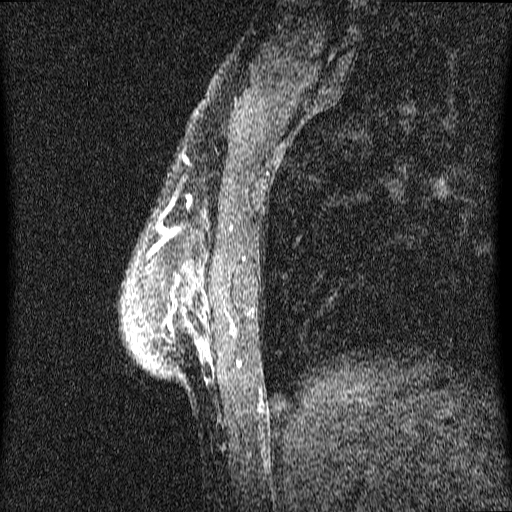
Breast MRI (dynamic contrast-enhanced), one sagittal slice. Slice 13 of 64 in the series (ordered by position). Dynamic contrast-enhanced series, image 2 of 4 at this slice position (ordered by acquisition). 1.5 T. TE 4.2 ms, TR 9.1 ms. 2 mm slice thickness. 512 × 512 image matrix, field of view 180 × 180 mm. Patient: female, 33 years.
Structures marked on this image (semi-automatic segmentation, software-assisted and operator-edited):
- analysis volume of interest (the breast-tissue region the enhancement analysis was run in; not a lesion): bounding box [x1, y1, x2, y2] px = [122, 156, 259, 411]
- tumour enhancement mask (voxels above the 70 % enhancement threshold inside the analysis volume of interest): [170, 322, 172, 325]